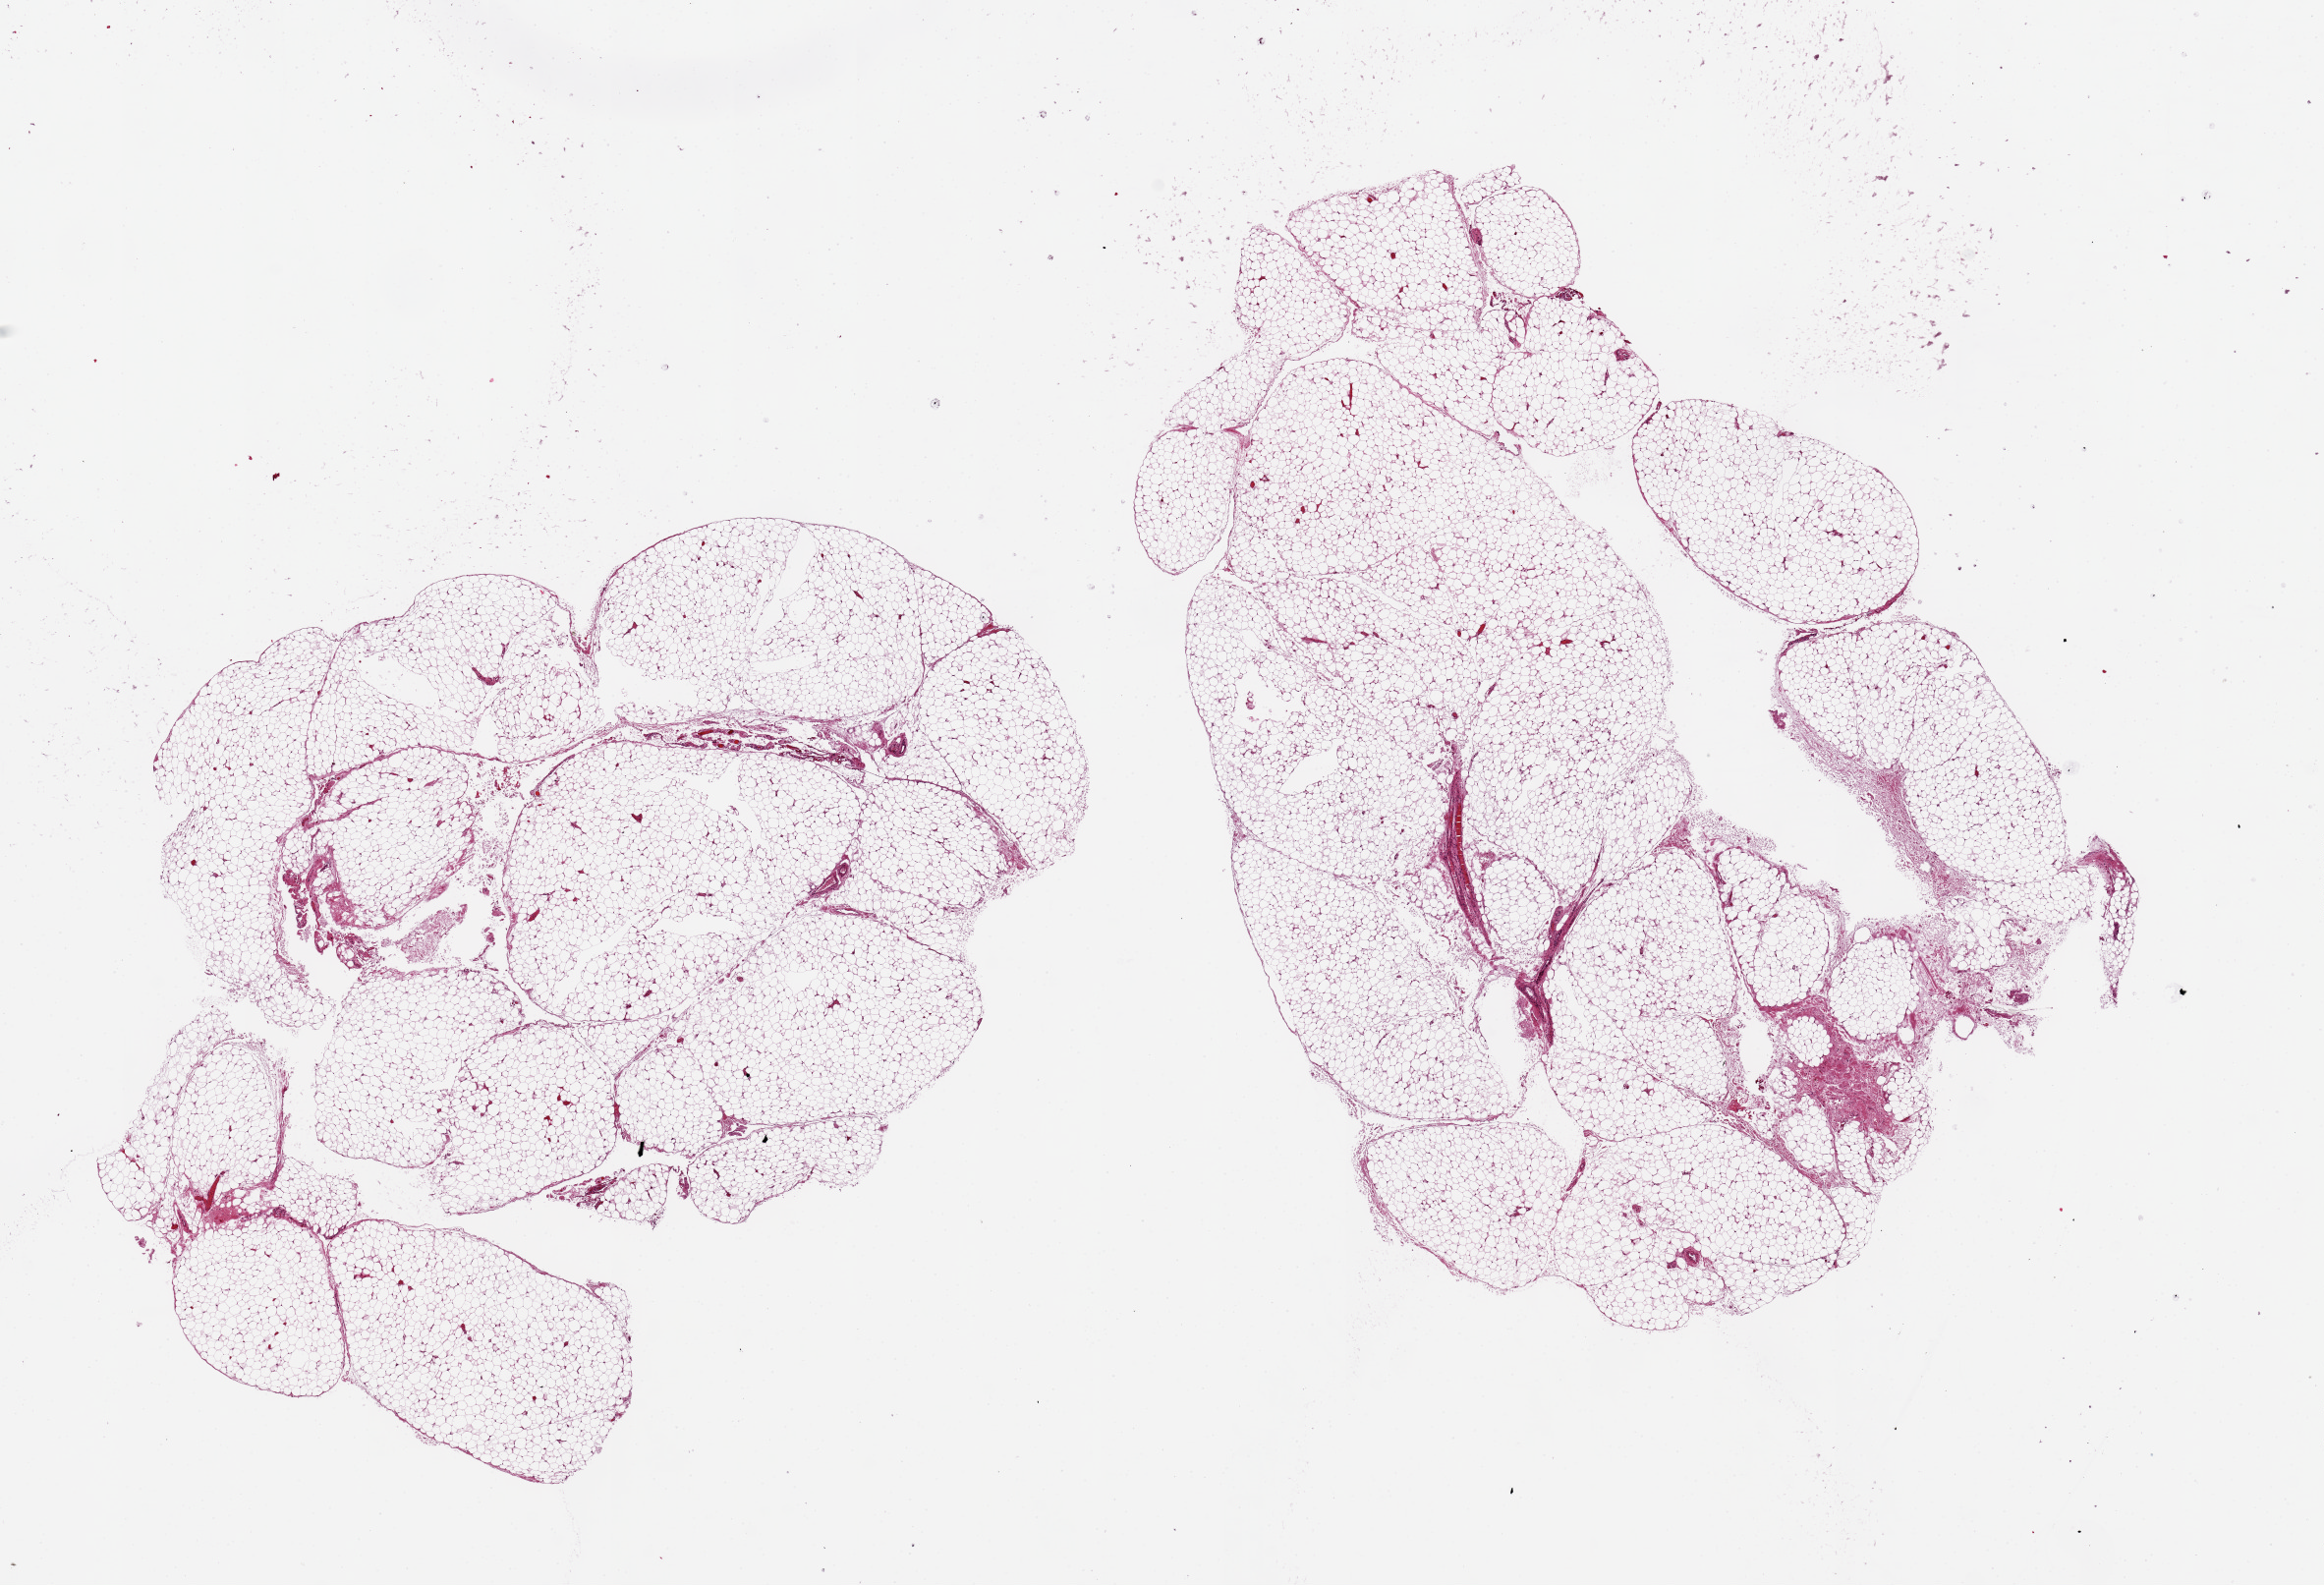
Digitized haematoxylin and eosin-stained section — a low-resolution overview of the entire scanned area, about 18.7 x 12.8 mm, PAXgene-fixed, paraffin-embedded tissue, target tissue: omentum, tissue donor sample. Donor: male.
Reviewer comment on this tissue sample: 2 pieces ~9x6mm.